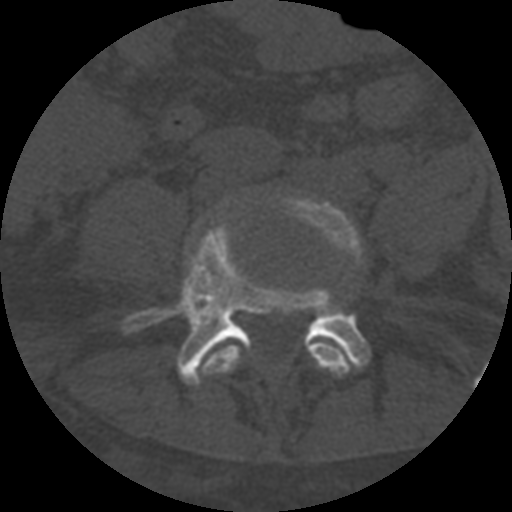
CT including the spine, one axial slice. Slice 194 of 708 in the series (ordered by position). Reconstruction kernel STANDARD. 120 kVp. One of 3 acquisitions stored at this slice position. Bone window (W 1800 / L 400 HU). 512 × 512 image matrix, field of view 160 × 160 mm. Patient age 55 years. From the clinical record (not read from this slice): primary cancer: colon; vertebrae with lytic lesions (as recorded): T12, L1, L5.
Outlined on this slice (semi-automatic segmentation, software-assisted and operator-edited):
- L4 vertebra: box from (x=202, y=195) to (x=362, y=376) px
- L5 vertebra: (x=123, y=225)–(x=371, y=386)